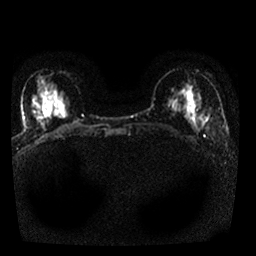
Breast MRI, one axial slice. Position 7 of 25 along the scan axis. Diffusion-weighted series; image 2 of 4 stored at this slice position (different b-values; order by instance number). 1.5 T. 4 mm slice thickness. 256 × 256 image matrix, field of view 330 × 330 mm. Female patient.
Structures marked on this image (expert manual segmentation):
- tumour on diffusion-weighted imaging: bounding box (x1, y1, x2, y2) in pixels: (202, 120, 206, 126)